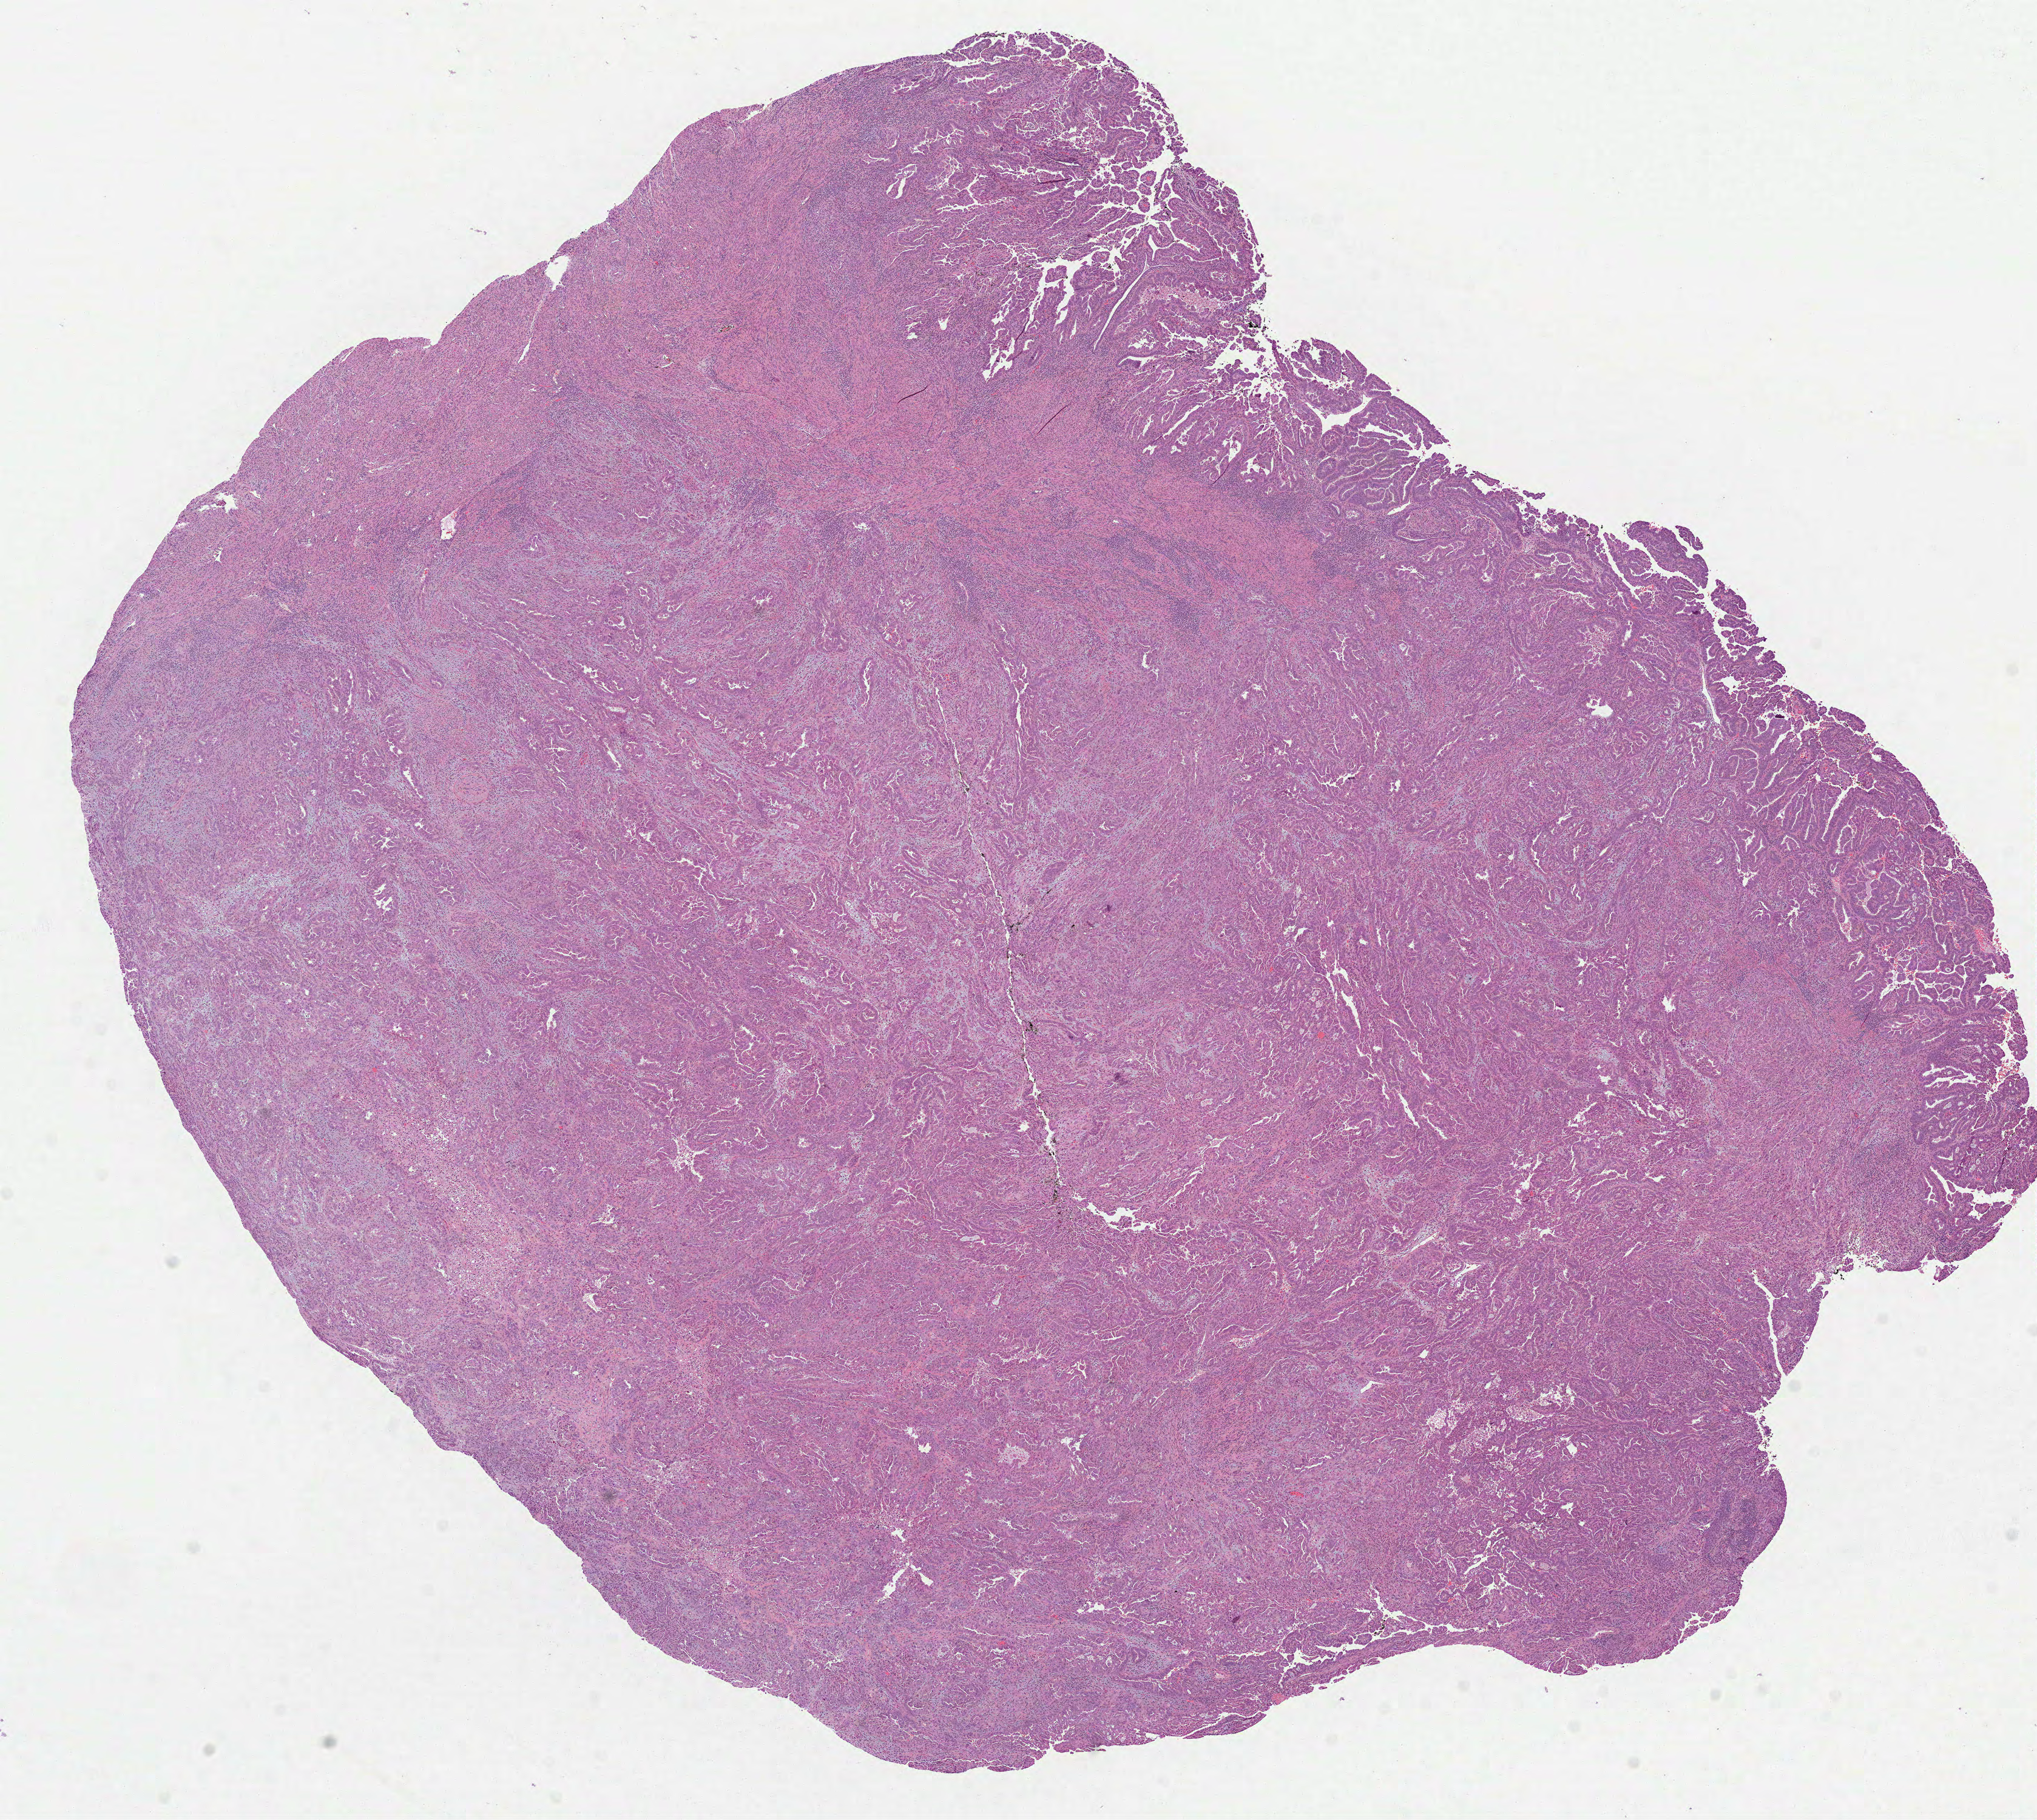
Whole-slide histology image, H&E-stained, whole scanned area (about 13.5 x 12.1 mm) shown as a low-resolution overview. Formalin-fixed paraffin-embedded (FFPE) diagnostic section. Primary tumour sample from the uterus. Female patient. Histologic grade: G3 (poorly differentiated).
FIGO stage: IB. Pathologic diagnosis: Endometrioid adenocarcinoma, NOS (endometrium).